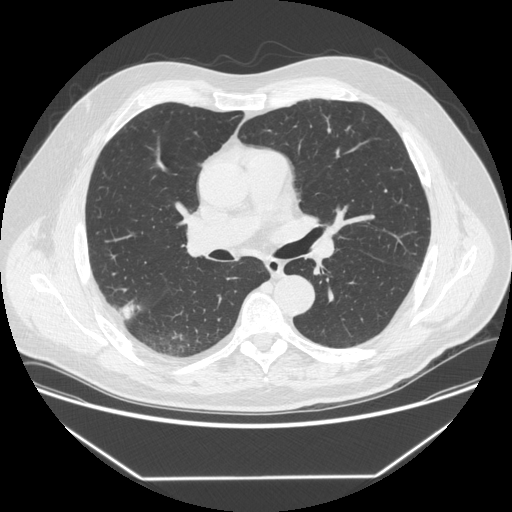
Low-dose screening chest CT, one axial slice; position 208 of 342 along the scan axis; reconstruction kernel STANDARD; 120 kVp; lung window (W 1500 / L -600 HU); 1.25 mm slice thickness; 512 × 512 image matrix, field of view 410 × 410 mm.
Structures marked on this image (expert manual segmentation):
- lesion 1 (tumor, upper lobe of right lung): bounding box <120,301,140,320> (left, top, right, bottom; pixels)